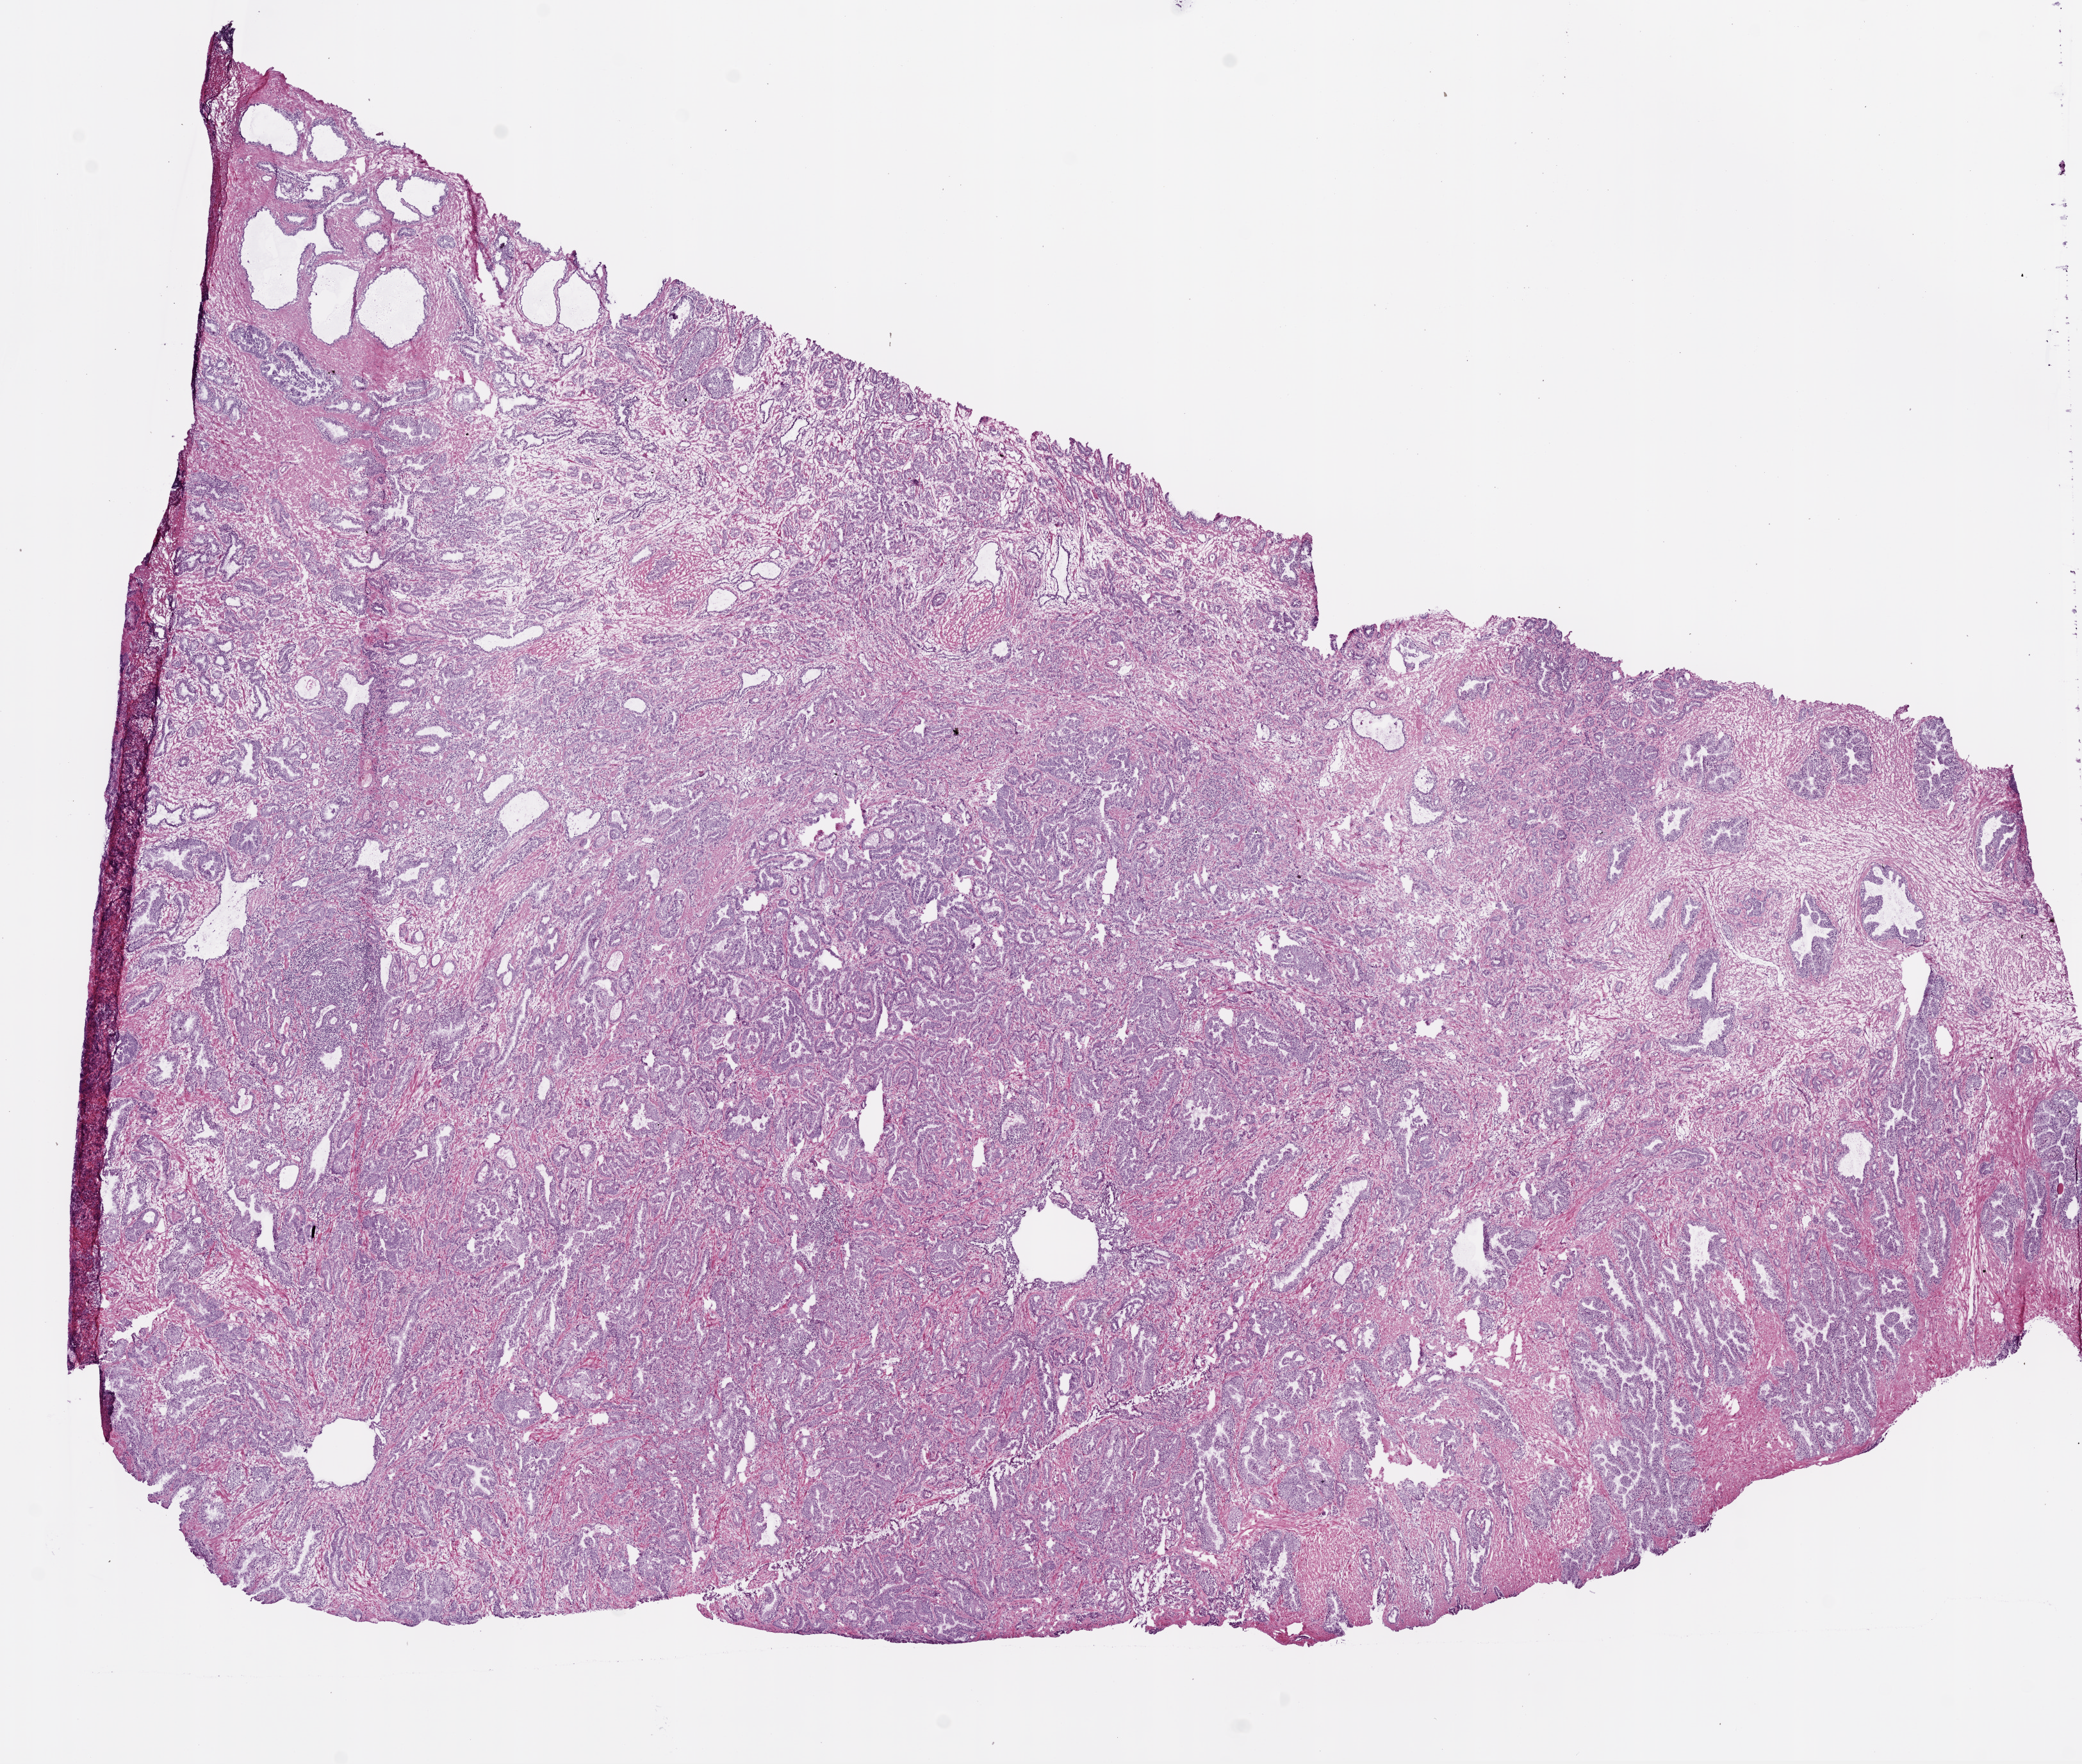
Hematoxylin and eosin (H&E) stained whole-slide image — low-resolution overview of the scanned area, about 13.0 x 11.0 mm. Frozen section from the bottom of the tissue portion. Prostate, primary tumour sample. Male, age 51 years at initial diagnosis. Gleason score: 7 (3+4). Composition of this section per pathologist review: tumour cells 65%, tumour nuclei 65%, normal cells 15%, stromal cells 20%, necrosis 0%. Inflammatory infiltration, as recorded: lymphocyte infiltration 2%, monocyte infiltration 0%, neutrophil infiltration 0%.
- lymph nodes positive (case pathology): 0 of 22 examined
- pathologic diagnosis: Acinar cell carcinoma (prostate gland)
- laterality: bilateral